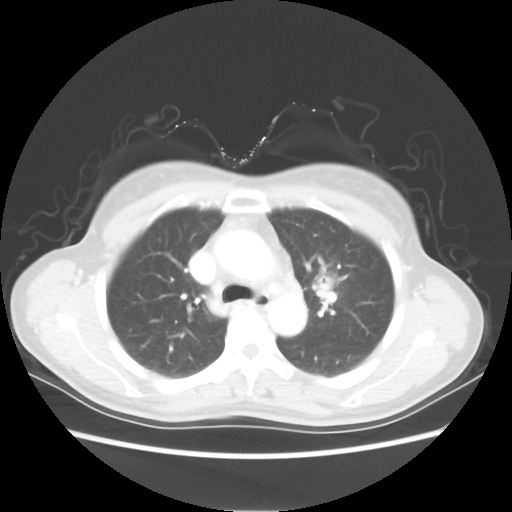
Chest CT, one axial slice; slice 38 of 54 in the series (ordered by position); reconstruction kernel STANDARD; 80 kVp; lung window (W 1500 / L -600 HU); 5 mm slice thickness; 512 × 512 image matrix. Female patient, age 53 years. Case-level facts recorded for this patient, not image findings: clinical TNM (as recorded): T1c N0 M0.
Outlined on this slice (bounding box drawn by a radiologist):
- lung tumour (recorded histology: adenocarcinoma): box from (x=304, y=259) to (x=350, y=312) px